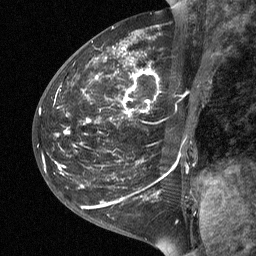
Breast MRI (dynamic contrast-enhanced), one sagittal slice; slice 23 of 64 in the series (ordered by position); dynamic contrast-enhanced study with each time point stored as its own series, time point 2 of 3 at this slice position (early post-contrast, ordered by acquisition time); 1.5 T; TE 4.8 ms, TR 27 ms; 2 mm slice thickness; 256 × 256 image matrix, field of view 200 × 200 mm. Female patient, age 42 years. From the clinical record (not read from this slice): setting: breast cancer imaged before/during neoadjuvant chemotherapy; receptor status: triple-negative.
Structures marked on this image (semi-automatically segmented with operator editing):
- analysis volume of interest (the breast-tissue region the enhancement analysis was run in; not a lesion): bounding box (x1, y1, x2, y2) in pixels: (43, 29, 203, 190)
- tumour enhancement mask (voxels above the 90 % enhancement threshold inside the analysis volume of interest): (81, 53, 156, 188)